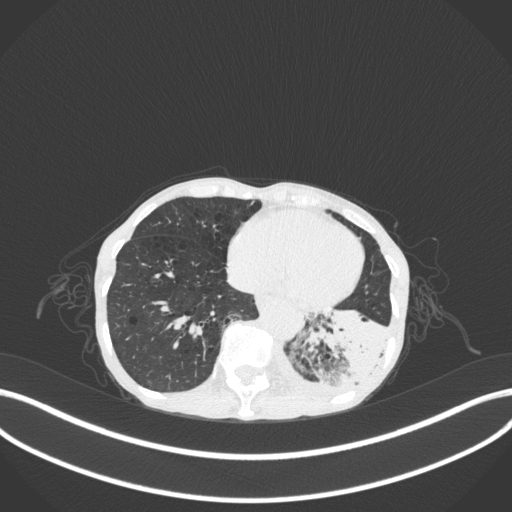
Chest CT, one axial slice; position 61 of 347 along the scan axis; lung window (W 1500 / L -600 HU); 512 × 512 image matrix, field of view 400 × 400 mm. Patient: female, 70 years. Case-level facts recorded for this patient, not image findings: clinical TNM (as recorded): T3 N0 M0; histopathological grade: G3.
Annotated regions visible in this slice (bounding box drawn by a radiologist):
- lung tumour (recorded histology: small cell carcinoma): bounding box <297,295,391,398> (left, top, right, bottom; pixels)